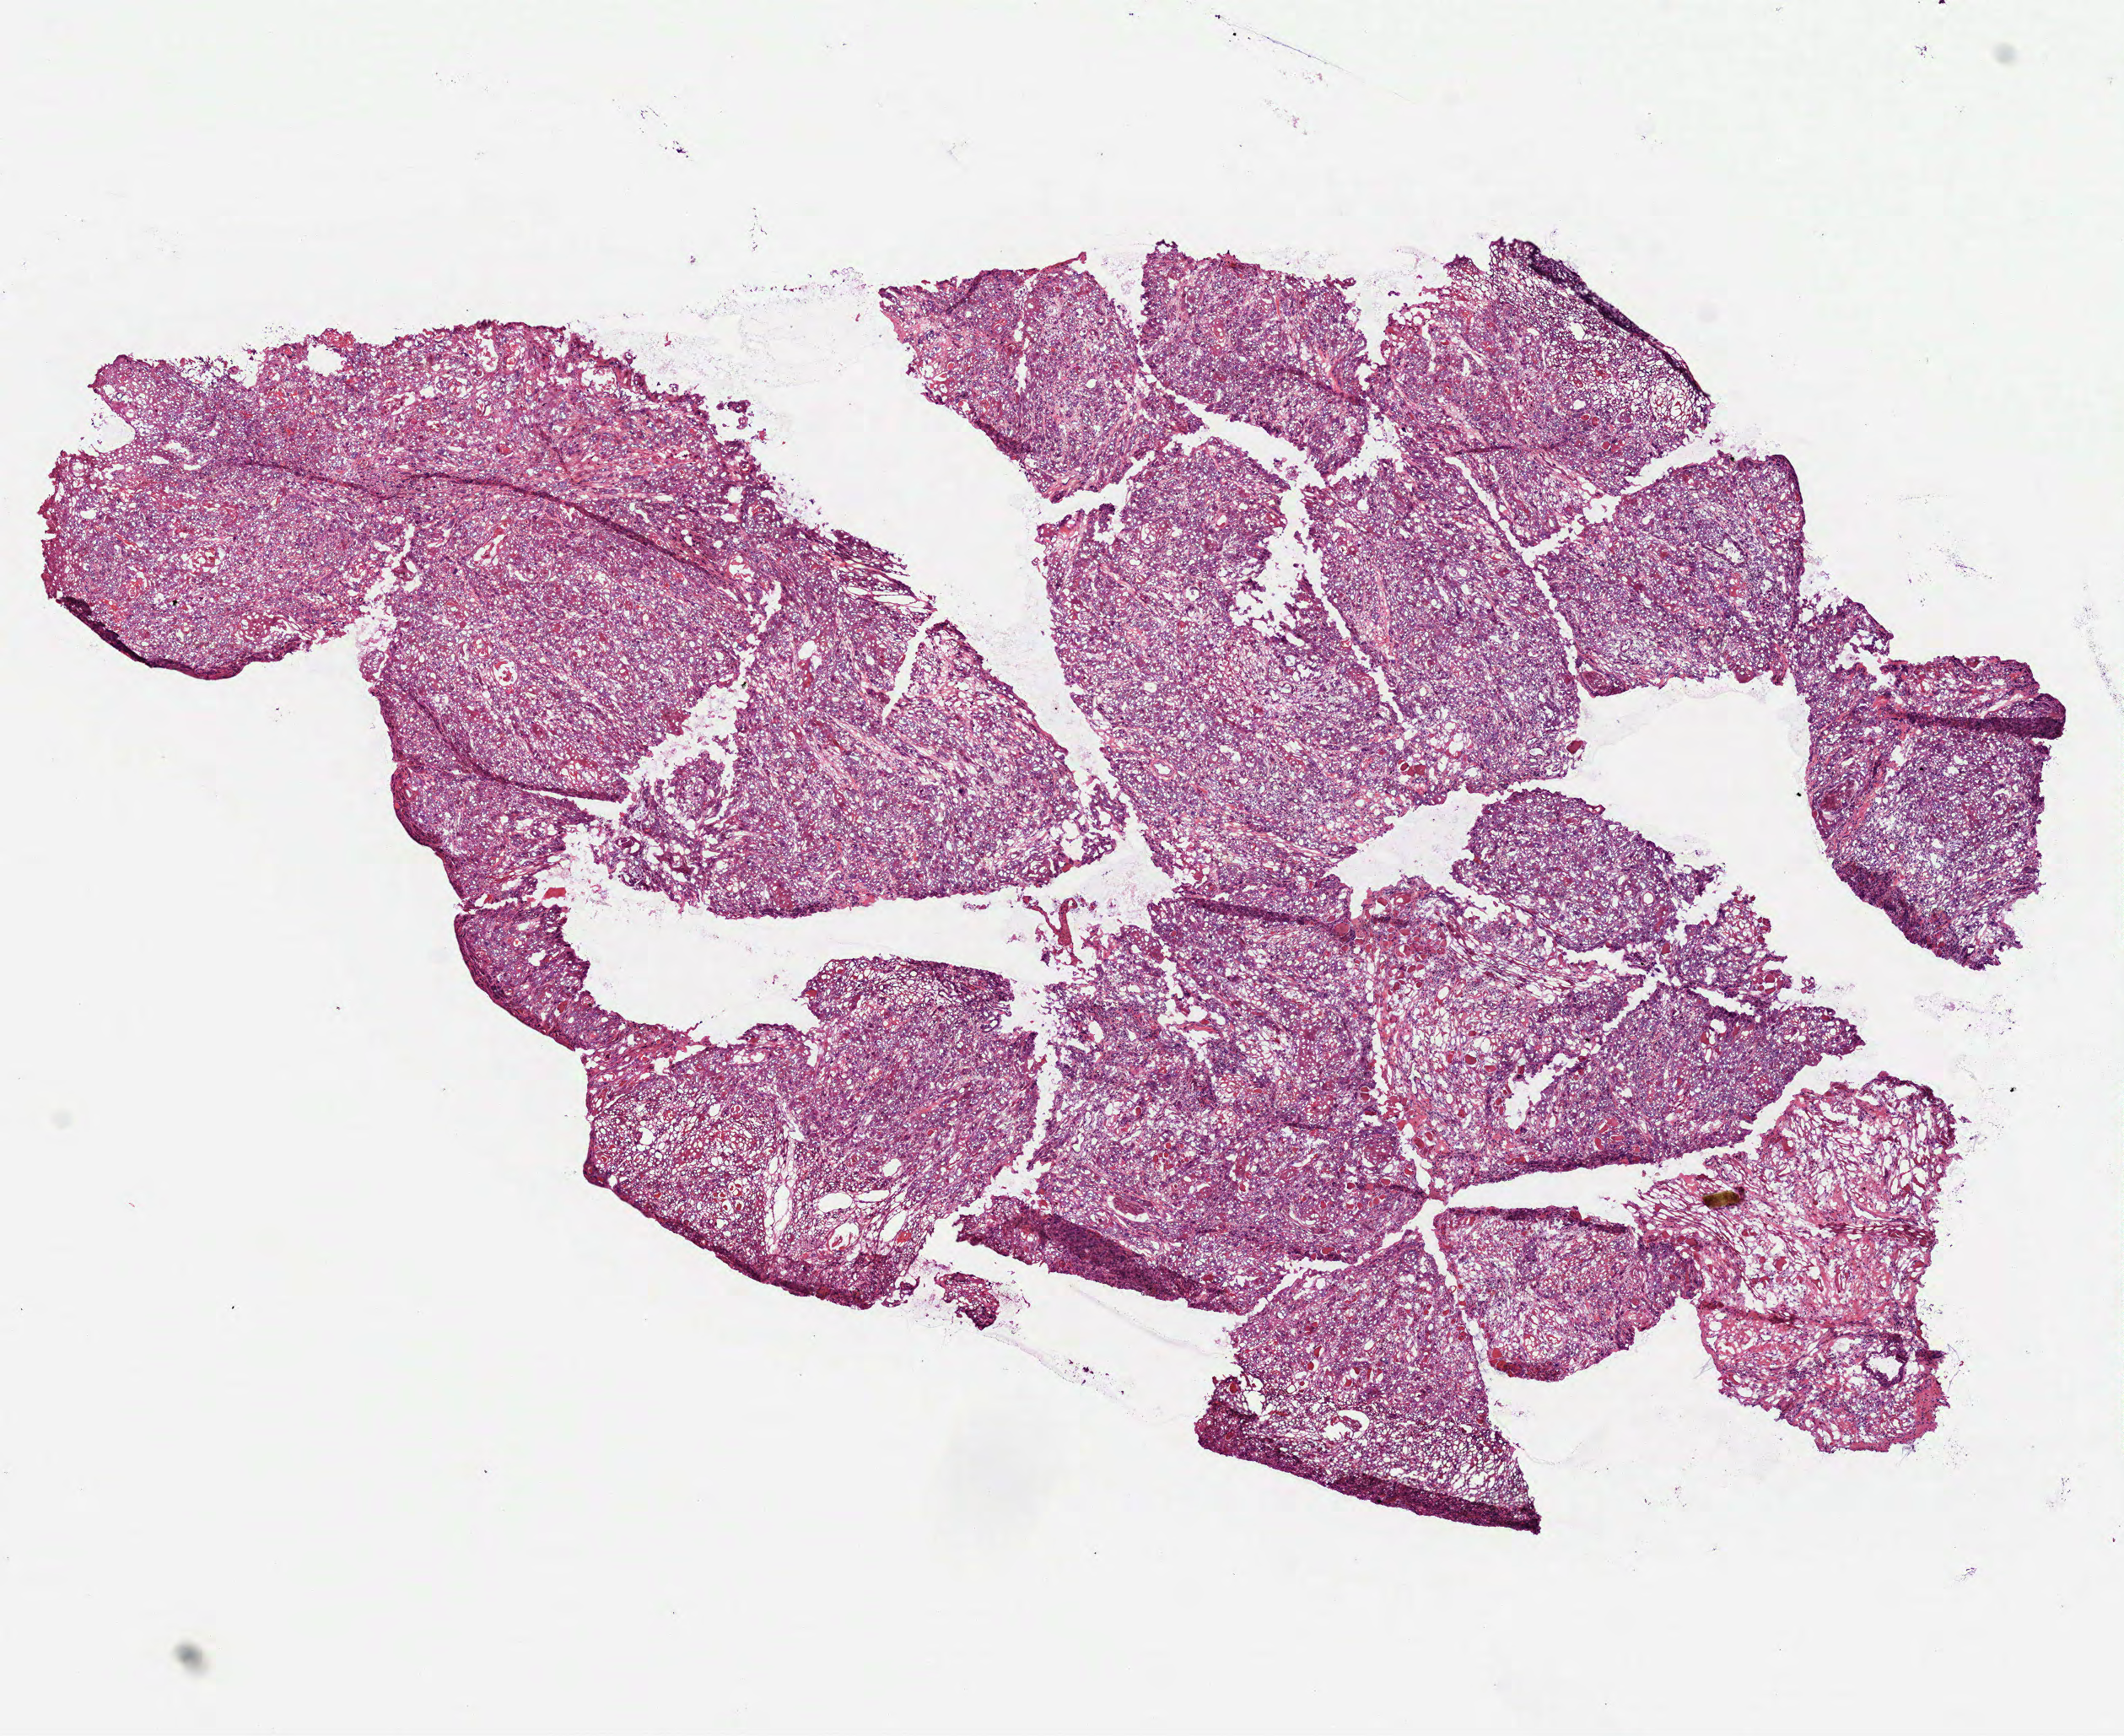
Whole-slide histology image, Hematoxylin and eosin (H&E) stained, whole scanned area (about 10.2 x 8.3 mm, from a 40x scan) shown as a low-resolution overview. Frozen section from the top of the tissue portion. Head and neck, primary tumour sample. Female patient; age at initial diagnosis 32 years. Histologic grade: G2 (moderately differentiated). Composition of this section per pathologist review: tumour cells 87%, tumour nuclei 85%, normal cells 3%, stromal cells 10%, necrosis 0%.
* AJCC pathologic stage: IVA
* histologic diagnosis: Squamous cell carcinoma, NOS (tongue, NOS)